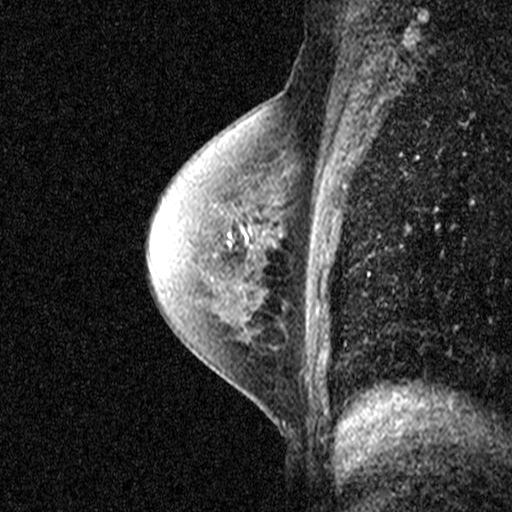
Breast MRI (dynamic contrast-enhanced), one sagittal slice; slice 25 of 40 in the series (ordered by position); dynamic contrast-enhanced study with each time point stored as its own series, time point 2 of 3 at this slice position (early post-contrast, ordered by acquisition time); 1.5 T; TE 4.5 ms, TR 11 ms; 3 mm slice thickness; 512 × 512 image matrix, field of view 200 × 200 mm. Female patient, age 55 years. Case-level facts recorded for this patient, not image findings: setting: breast cancer imaged before/during neoadjuvant chemotherapy; receptor status: HR-positive, HER2-negative.
Structures marked on this image (semi-automatic segmentation, software-assisted and operator-edited):
- analysis volume of interest (the breast-tissue region the enhancement analysis was run in; not a lesion): box from (x=194, y=202) to (x=279, y=277) px
- tumour enhancement mask (voxels above the 90 % enhancement threshold inside the analysis volume of interest): (x=243, y=232)–(x=248, y=245)